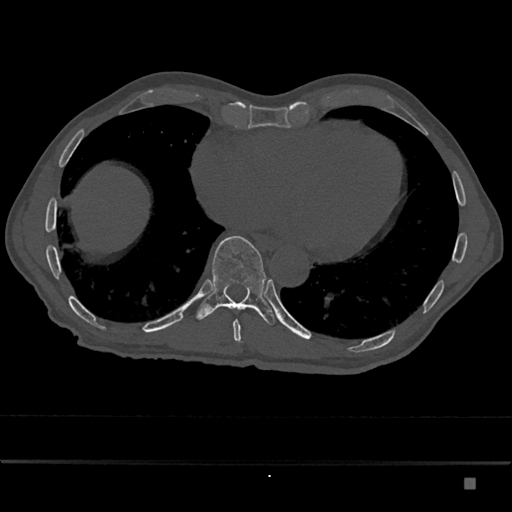
CT including the spine, one axial slice. Slice 759 of 797 in the series (ordered by position). Reconstruction kernel Br40s/3. Bone window (W 1800 / L 400 HU). 0.5 mm slice thickness. 512 × 512 image matrix, field of view 390 × 390 mm. Patient: male, 72 years. From the clinical record (not read from this slice): primary cancer: prostate.
Structures marked on this image (semi-automatic segmentation, software-assisted and operator-edited):
- T10 vertebra: bounding box [x1, y1, x2, y2] px = [196, 236, 276, 326]
- T9 vertebra: [233, 320, 242, 343]